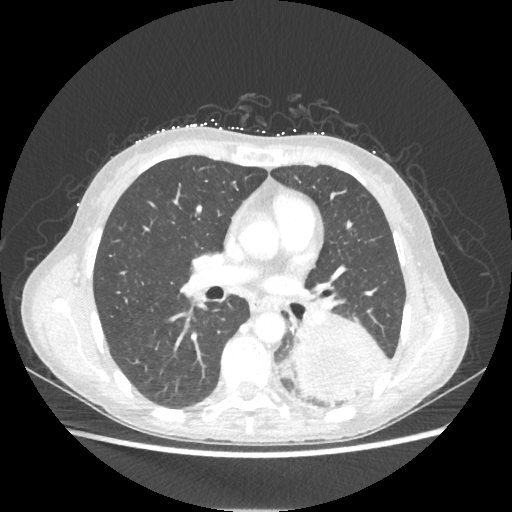
Chest CT, one axial slice. Position 117 of 221 along the scan axis. Lung window (W 1500 / L -600 HU). 1.25 mm slice thickness. 512 × 512 image matrix, field of view 360 × 360 mm. Patient: female, 53 years. Case-level facts recorded for this patient, not image findings: clinical TNM (as recorded): T3 N0 M0.
Outlined on this slice (rectangle marked by the reading radiologist):
- lung tumour (recorded histology: adenocarcinoma): bounding box [x1, y1, x2, y2] px = [290, 311, 387, 404]